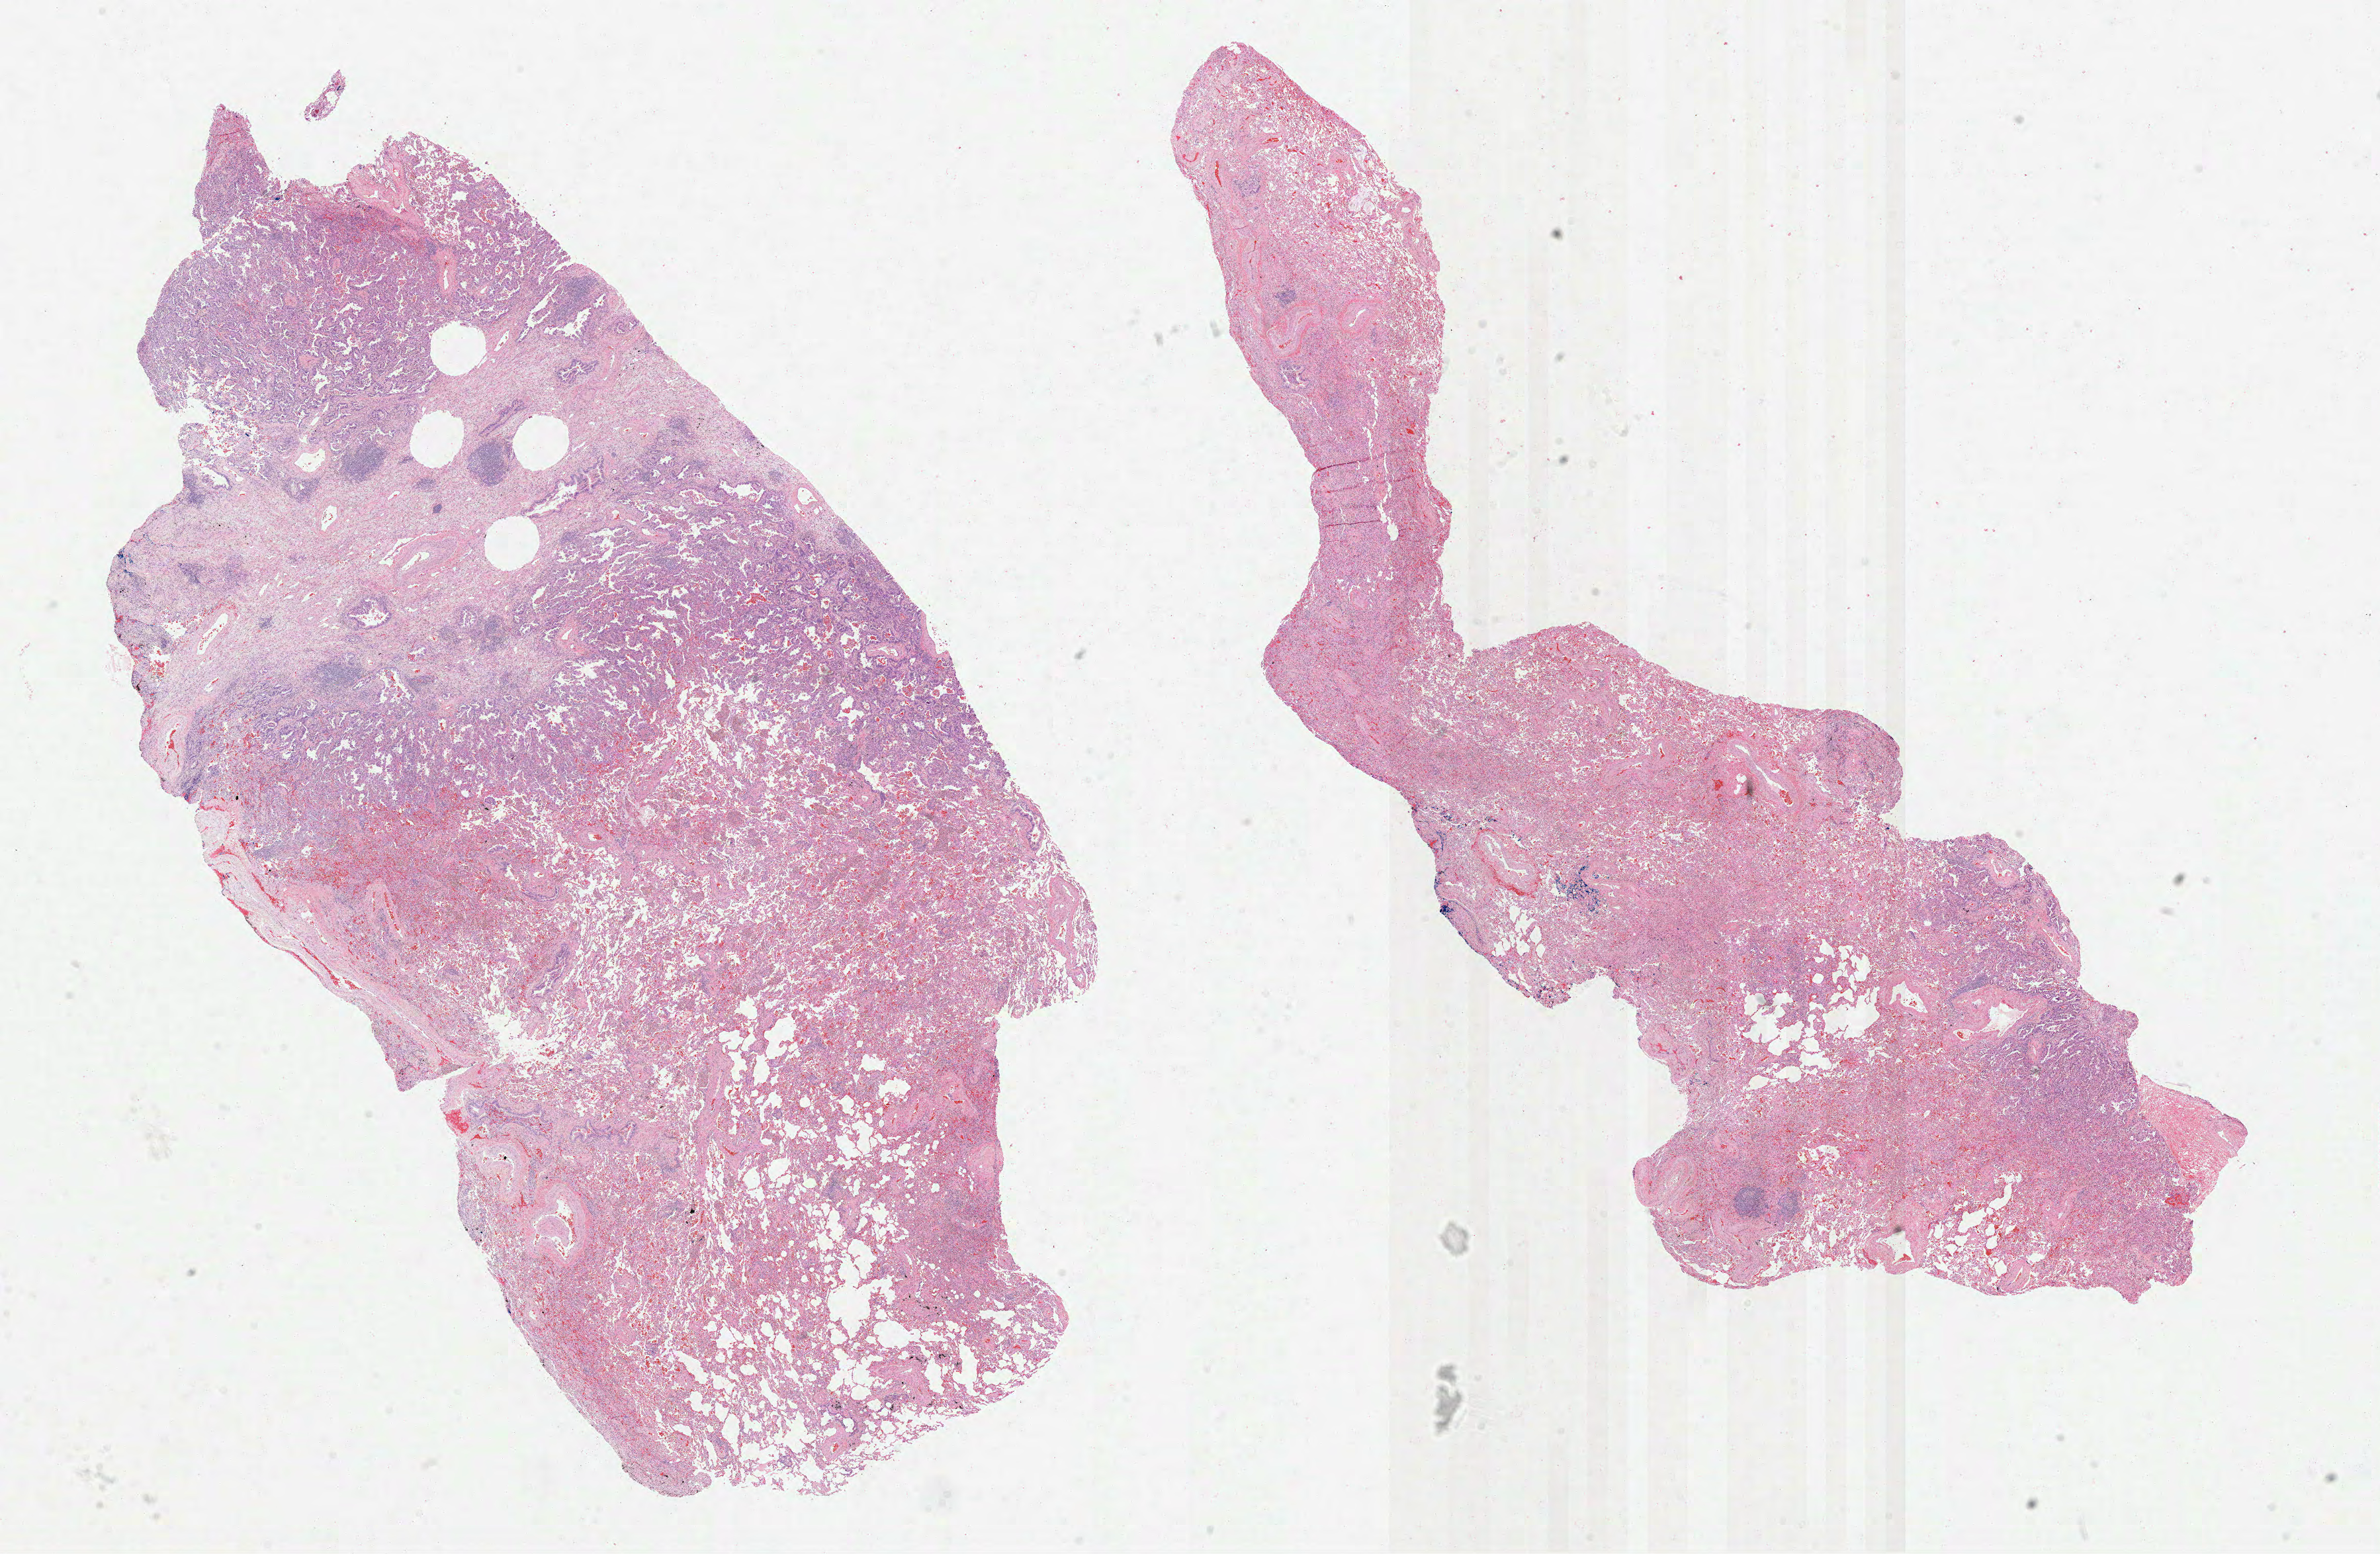
Whole-slide histology image, Hematoxylin and eosin (H&E) stained — low-resolution overview of the scanned area, about 29.0 x 18.9 mm (acquisition: 40x scan), FFPE section, sample: primary tumour, lung. Female, age 58 years at initial diagnosis.
AJCC pathologic stage: IA (7th edition). Laterality: right. Diagnosis: Bronchiolo-alveolar carcinoma, non-mucinous.